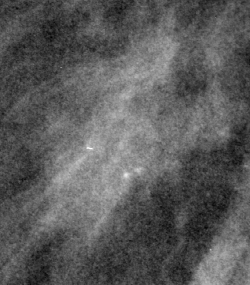
Region of interest cut from a scanned film mammogram (one marked finding), right breast, MLO view, BI-RADS breast density category 3 (scale 1–4).
- Marked abnormality: mass, shape irregular, margins spiculated; BI-RADS assessment category 4; pathology result (as recorded, not read from the image): malignant.